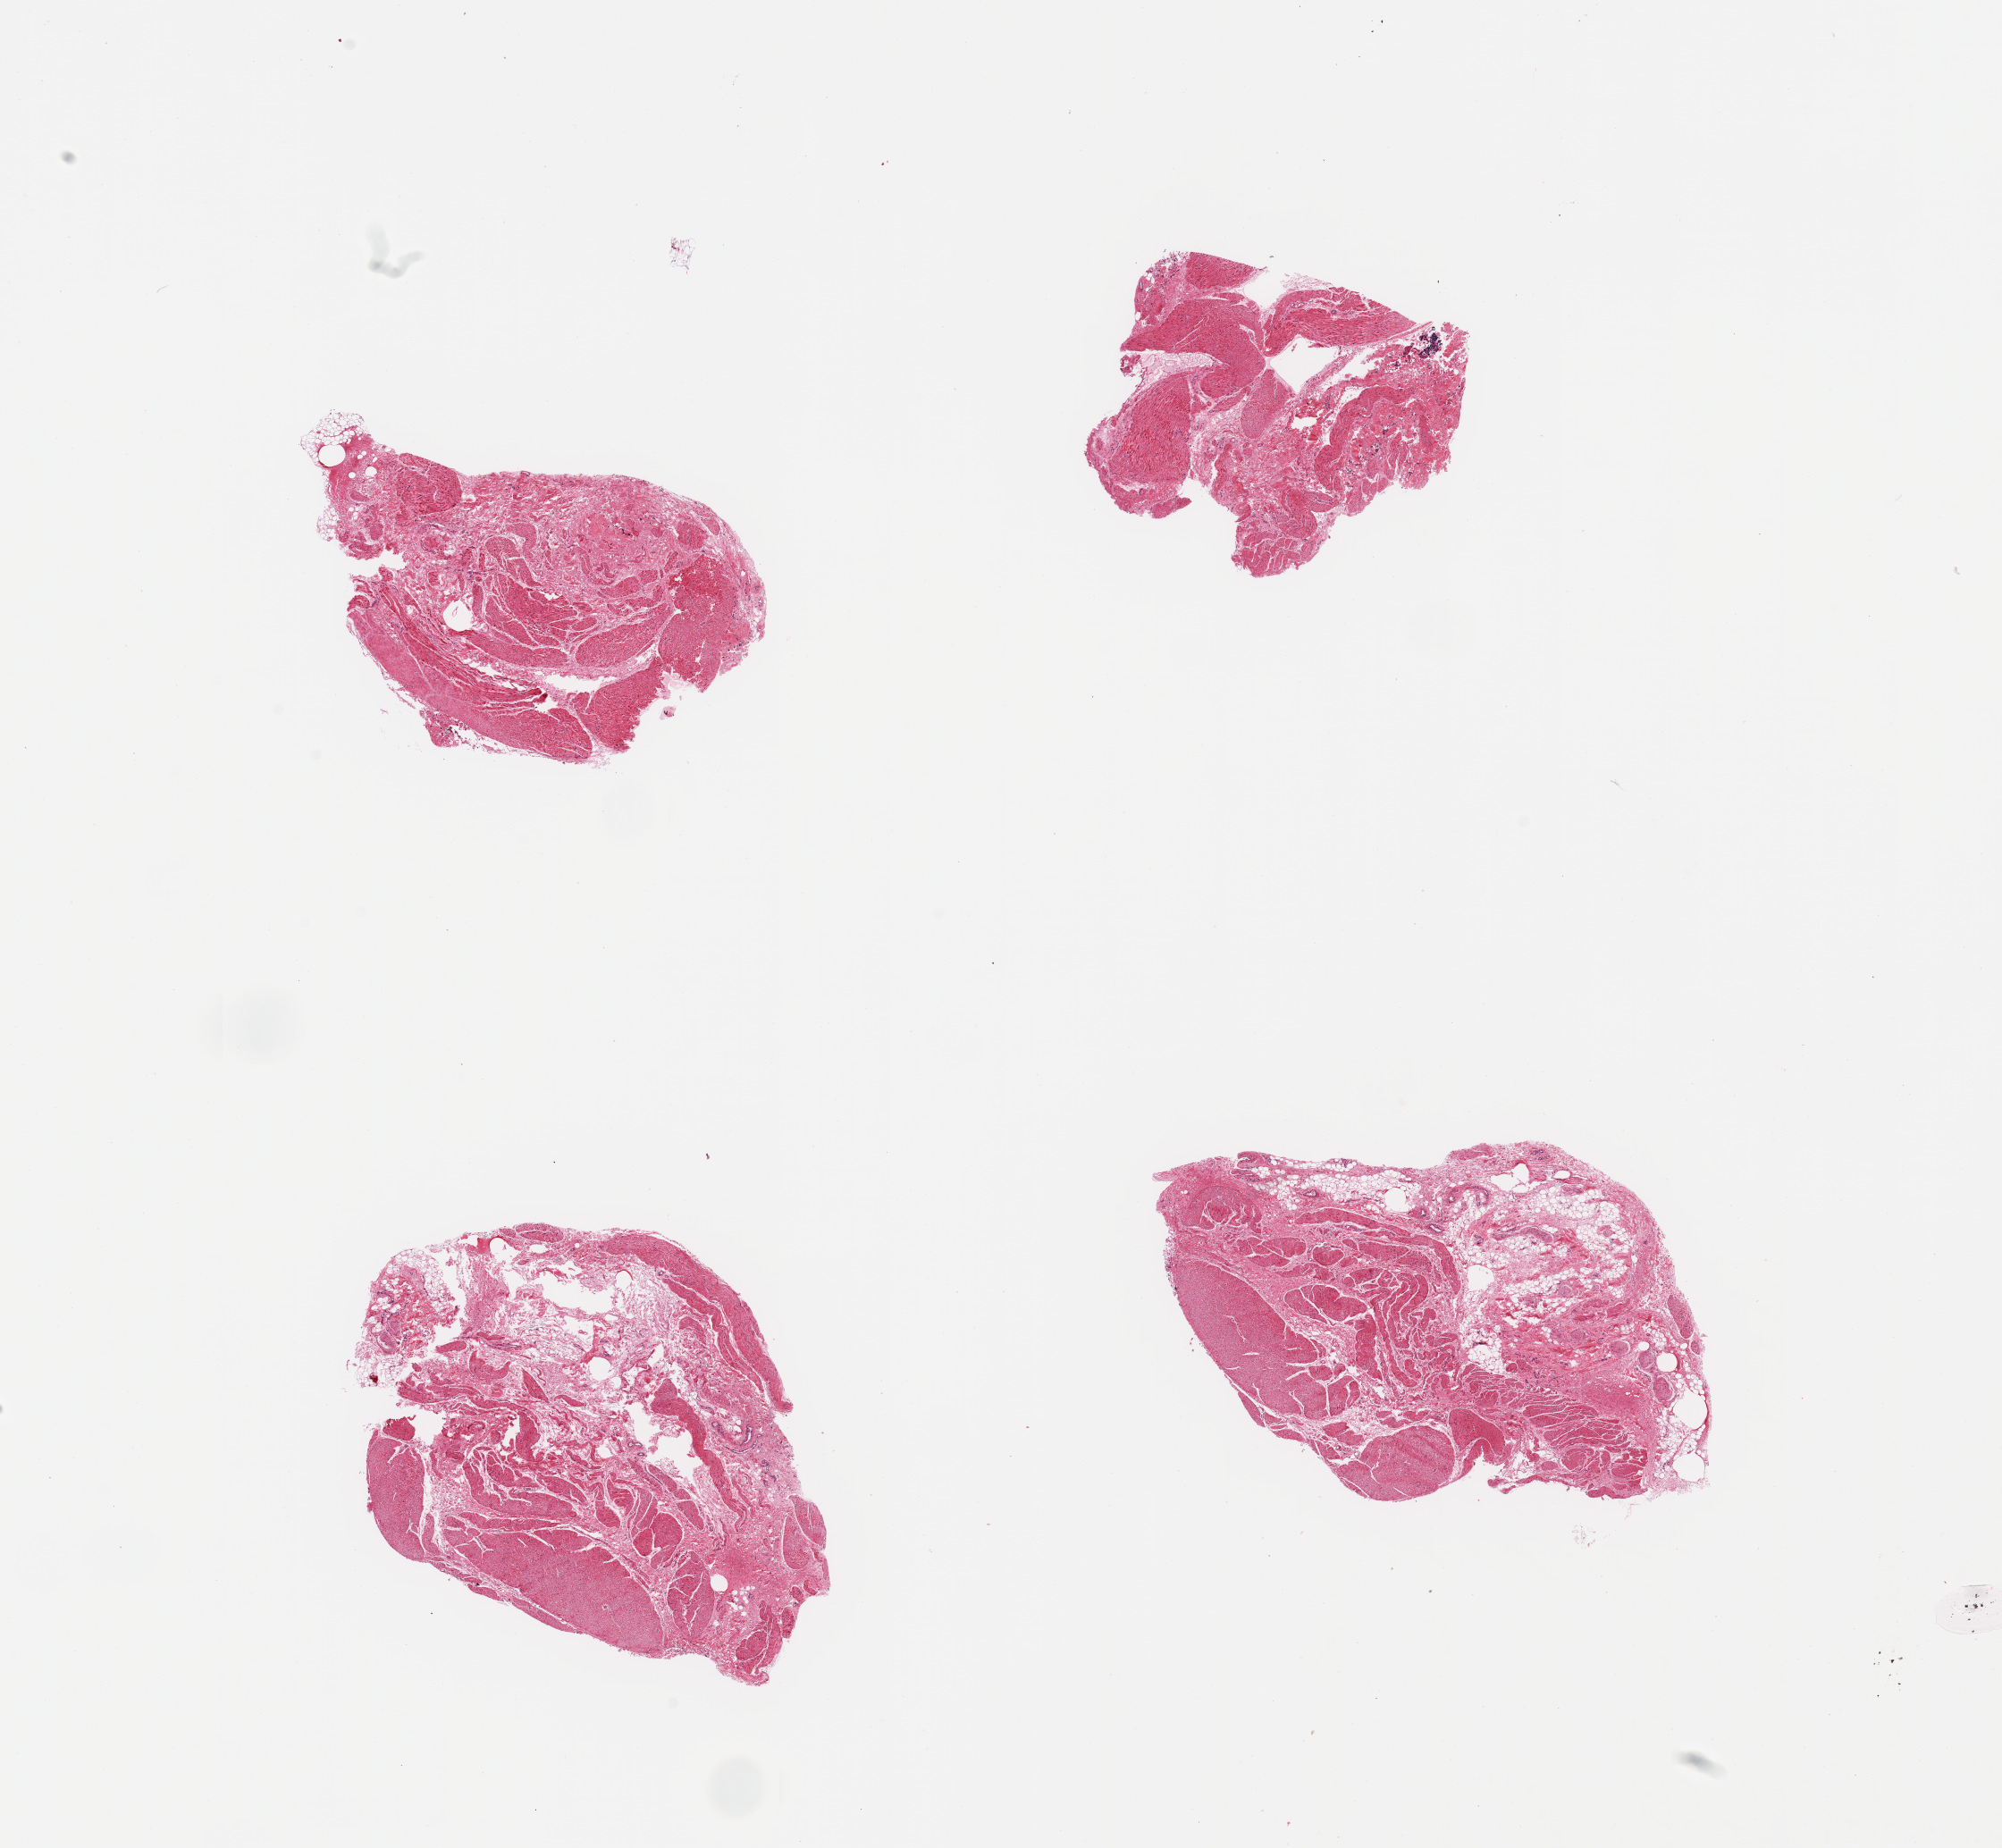
Digitized H&E-stained section — shown as a low-resolution overview of the whole scanned area (about 17.7 x 16.4 mm). PAXgene-fixed, paraffin-embedded tissue. Sampled site (target tissue): esophageal muscle. Donor tissue sample. Donor sex: male.
- review note (as recorded): 4 pieces; high stromal content [up to 50%]